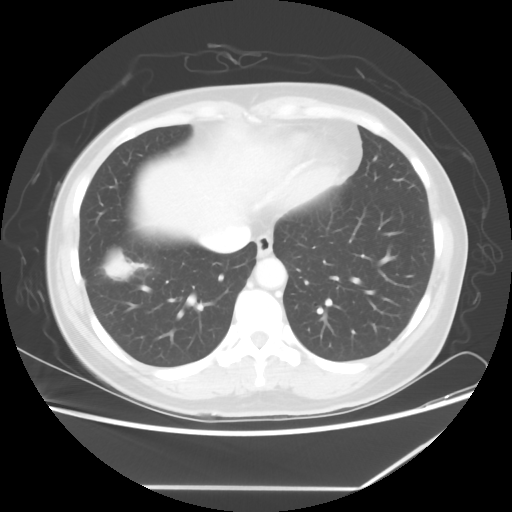
Chest CT, one axial slice; slice 19 of 60 in the series (ordered by position); lung window (W 1500 / L -600 HU); 5 mm slice thickness; 512 × 512 image matrix, field of view 374 × 374 mm. Patient: female, 42 years. Case-level facts recorded for this patient, not image findings: clinical TNM (as recorded): T2 N1 M0.
Annotated regions visible in this slice (bounding box drawn by a radiologist):
- lung tumour (recorded histology: adenocarcinoma): bounding box [x1, y1, x2, y2] px = [102, 248, 131, 281]